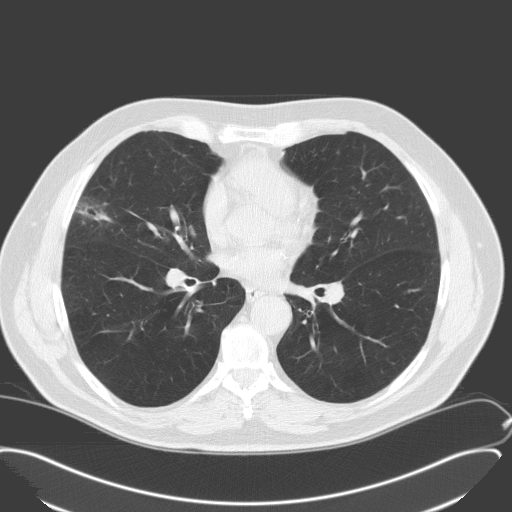
Axial slice from a low-dose chest CT screening exam; second annual screen; lung window (W 1500 / L -600 HU); 3.2 mm slice thickness; standard (soft-tissue) reconstruction kernel (C); 512 × 512 image matrix. Male participant, aged 65 years at enrolment.
Lesion marked by an expert reader, bounding box (x1, y1, x2, y2) in pixels: (55, 191, 116, 244). Screening reader's record for this exam: no non-calcified nodule ≥4 mm recorded. Participant outcome: lung cancer diagnosed 346 days after this screen — adenocarcinoma, NOS, right middle lobe, moderately differentiated (G2), stage IA (AJCC 6th edition), 25 mm at pathology.